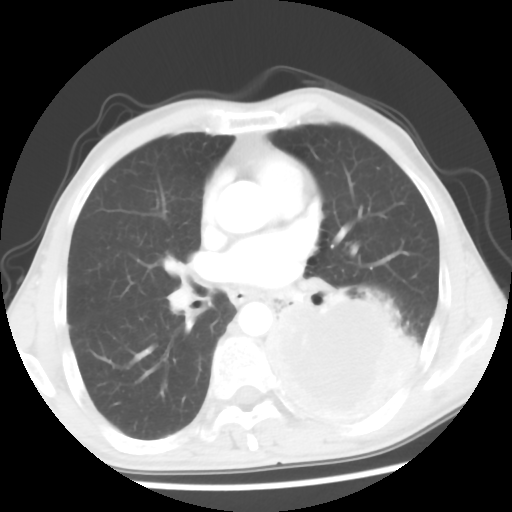
Chest CT, one axial slice; position 29 of 56 along the scan axis; lung window (W 1500 / L -600 HU); 512 × 512 image matrix, field of view 318 × 318 mm. Patient: male, 60 years. From the clinical record (not read from this slice): clinical TNM (as recorded): T4 N0 M0.
Outlined on this slice (bounding box drawn by a radiologist):
- lung tumour (recorded histology: squamous cell carcinoma): box from (x=250, y=282) to (x=434, y=446) px